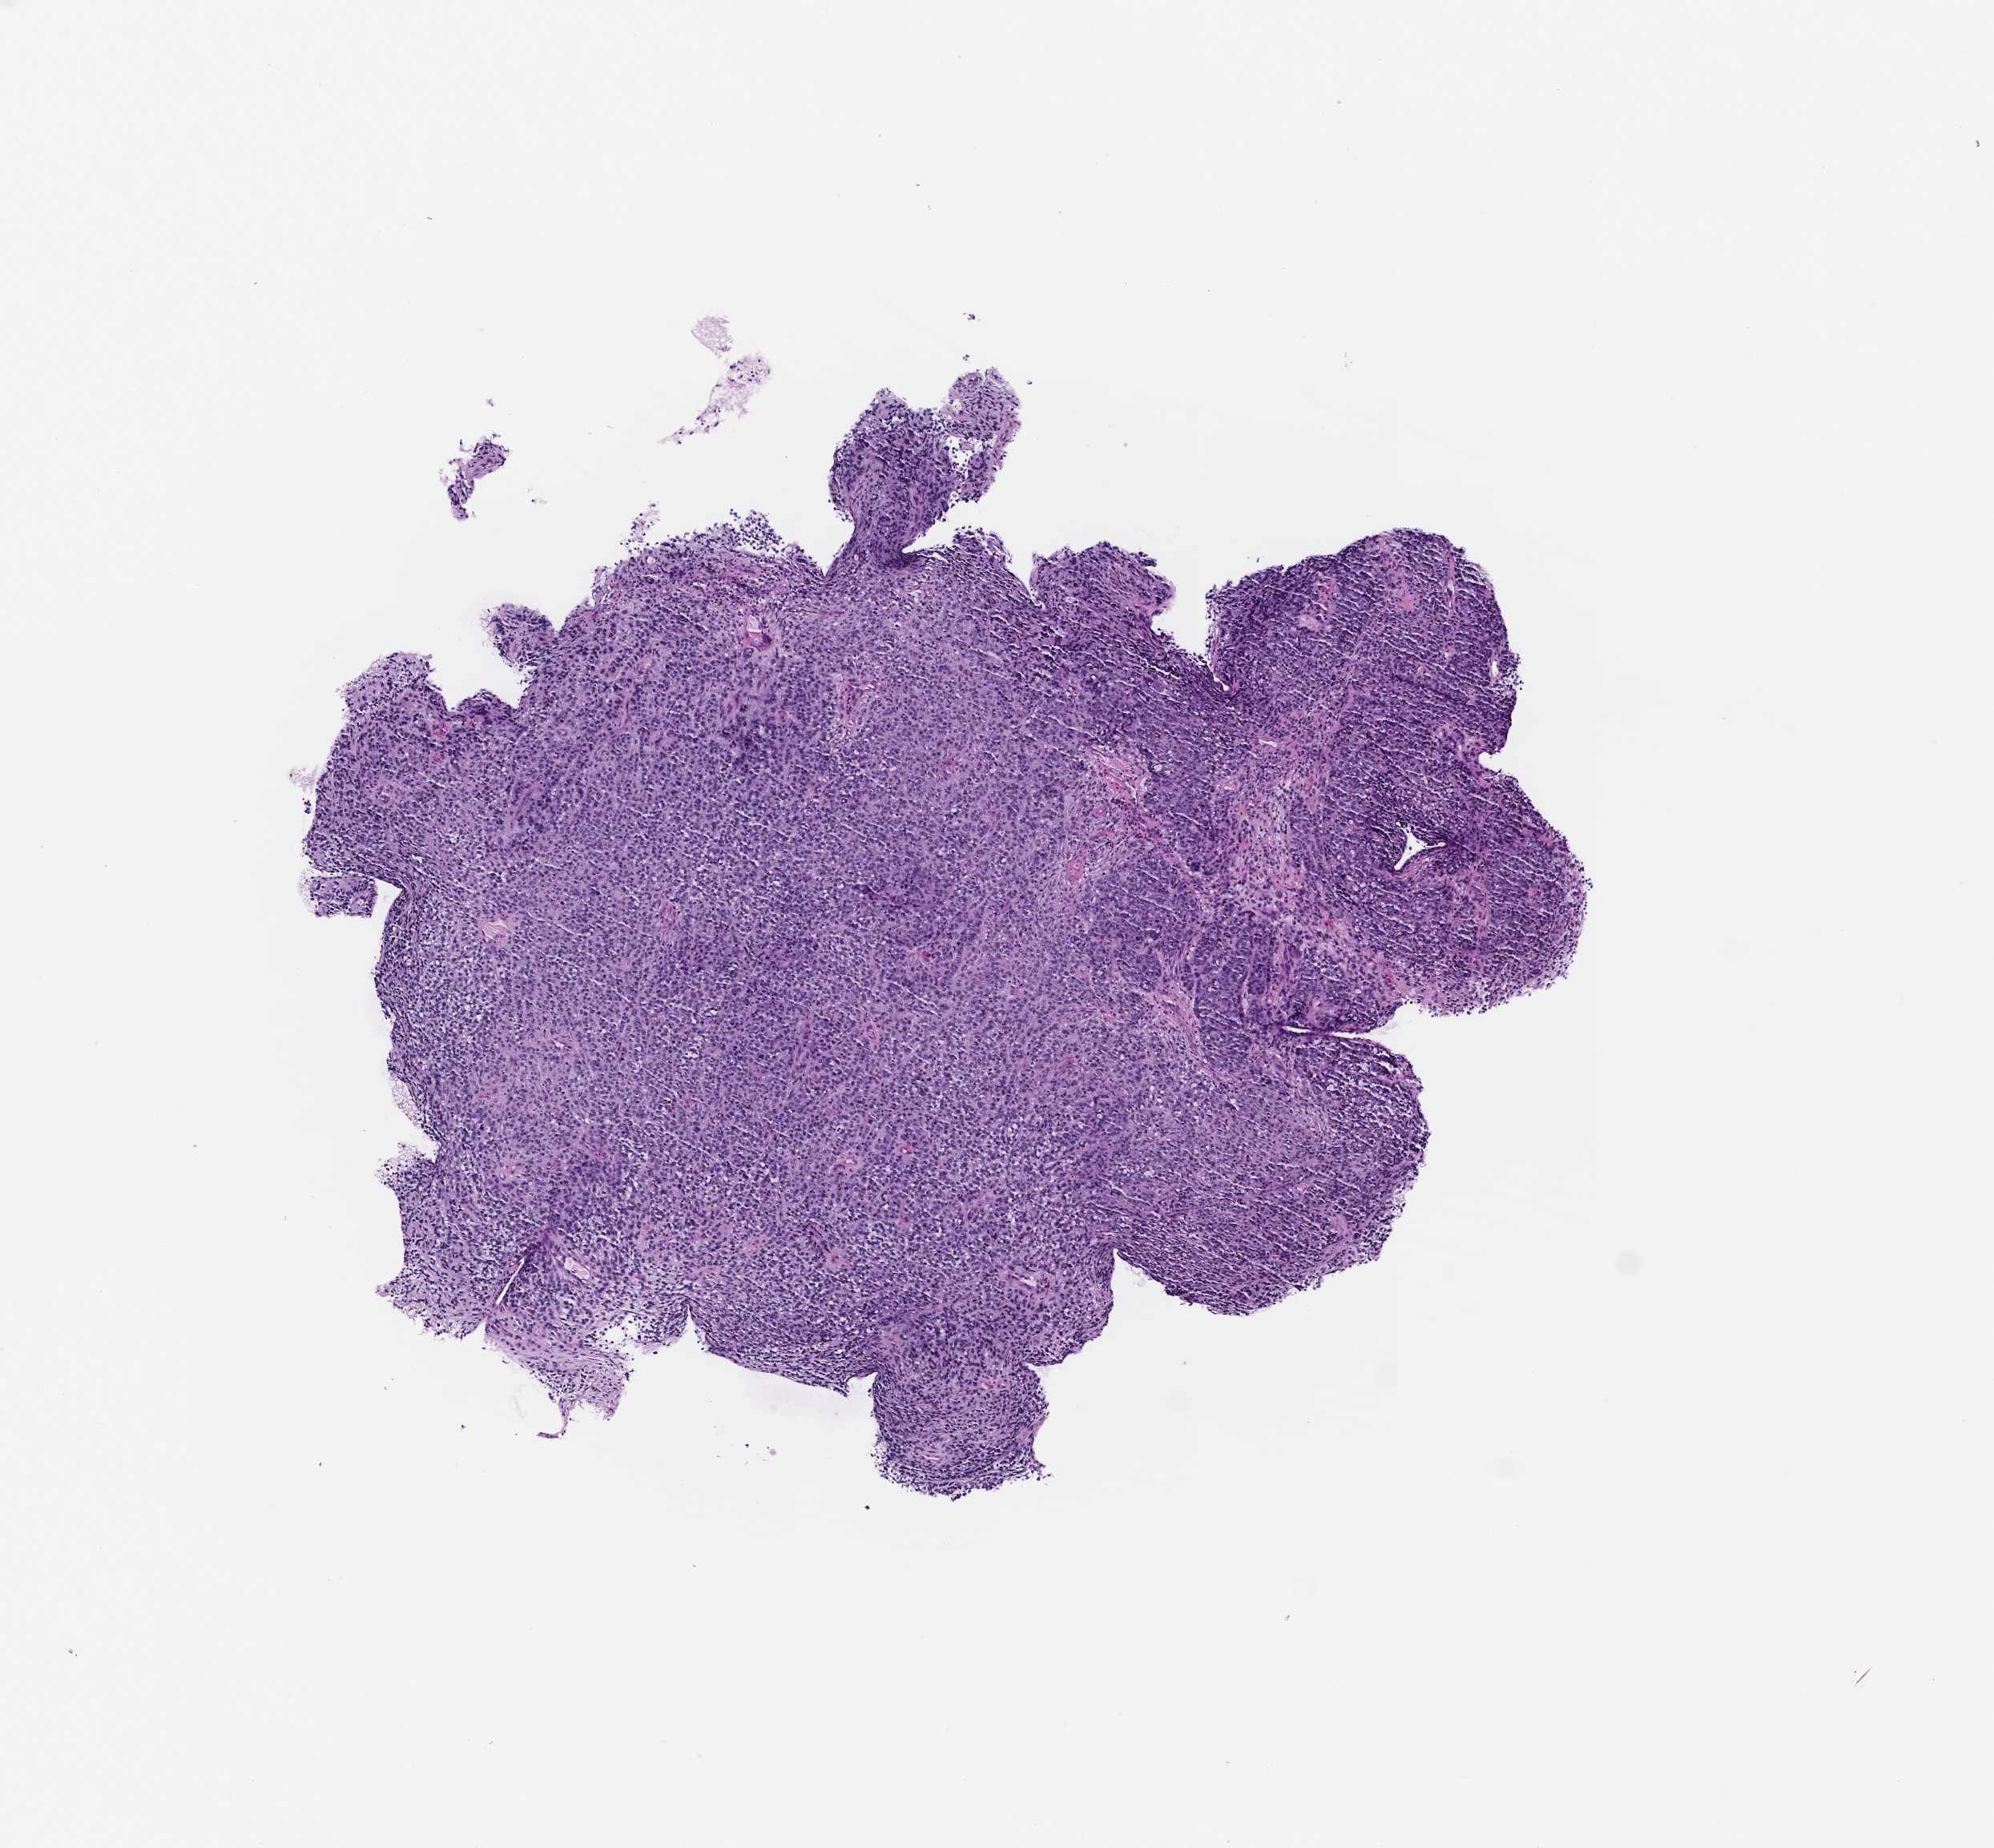
H&E whole-slide image — low-resolution overview of the scanned area, about 5.0 x 4.7 mm. FFPE section. Site: skin. Specimen time point: collected at baseline (before treatment). Female patient.
This section: primary tumour tissue. Diagnosis: Melanoma.